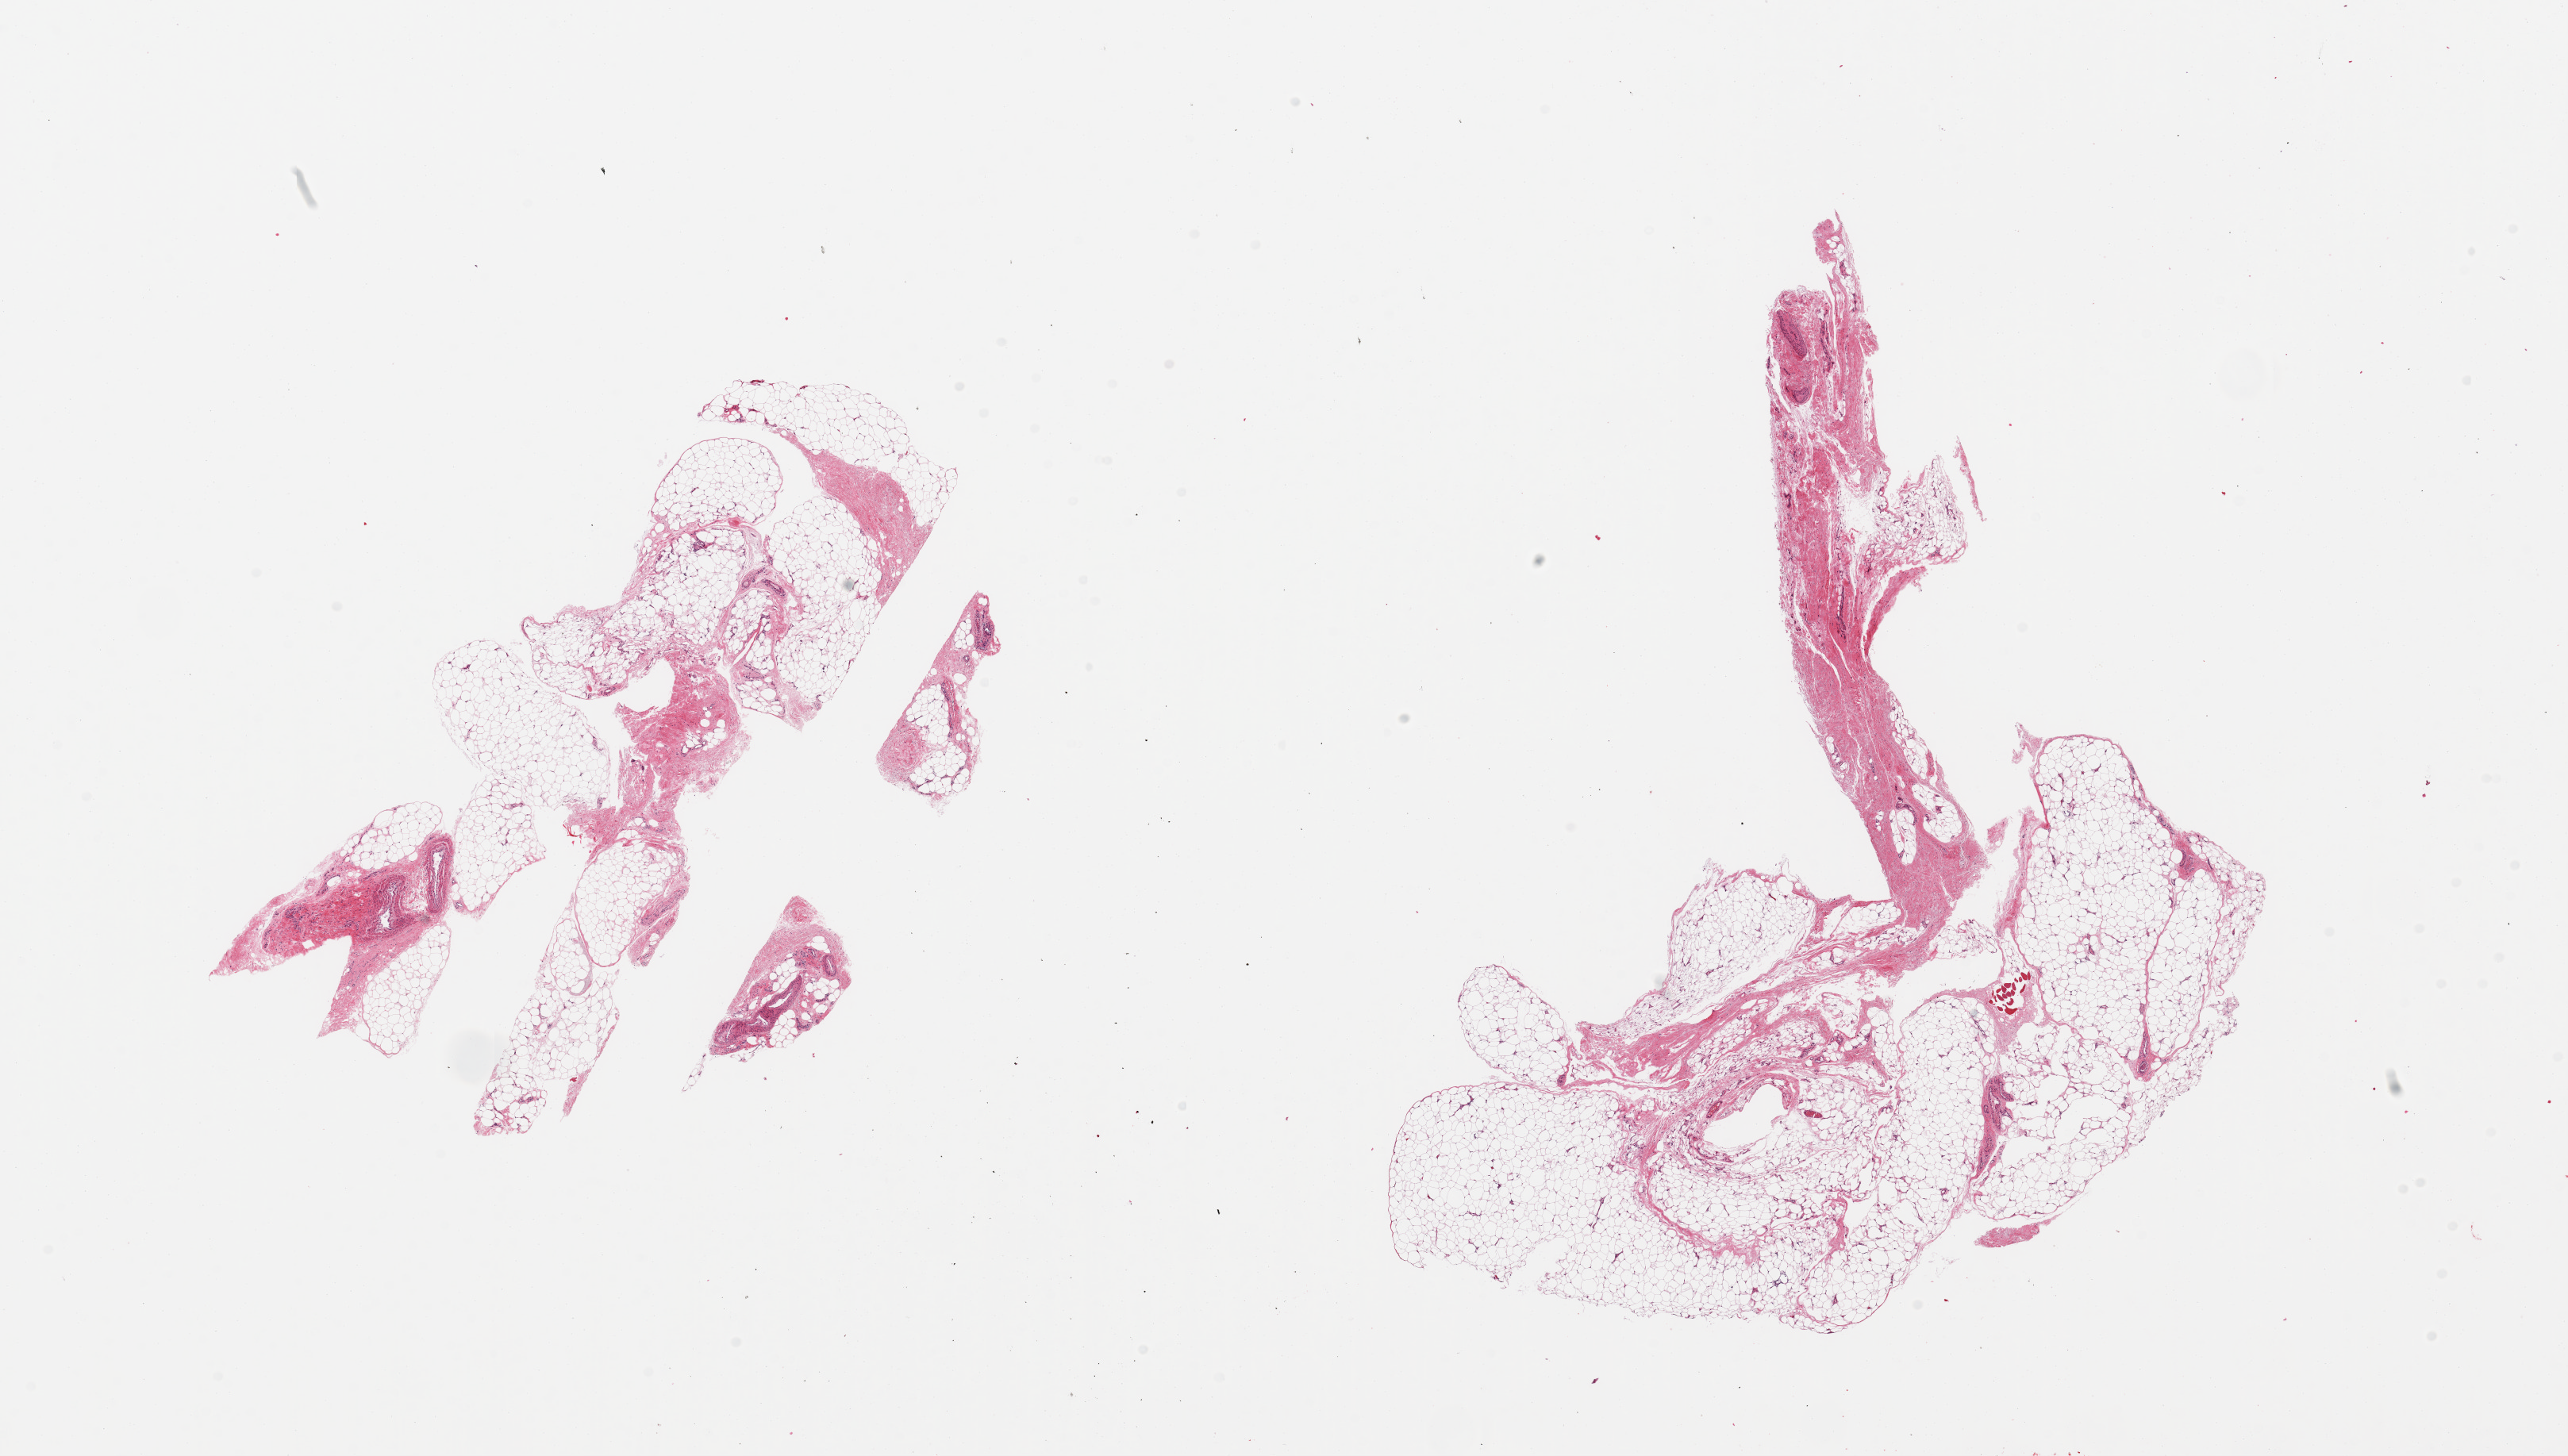
Digitized haematoxylin and eosin-stained section, brightfield — low-resolution overview of the scanned area, about 25.6 x 14.5 mm, PAXgene-fixed paraffin-embedded (PFPE) section, target tissue: adipose tissue, donor tissue sample. Female donor.
• review note (as recorded): 2 pieces, ~30-40% fascia/vascular elements-sample with caution